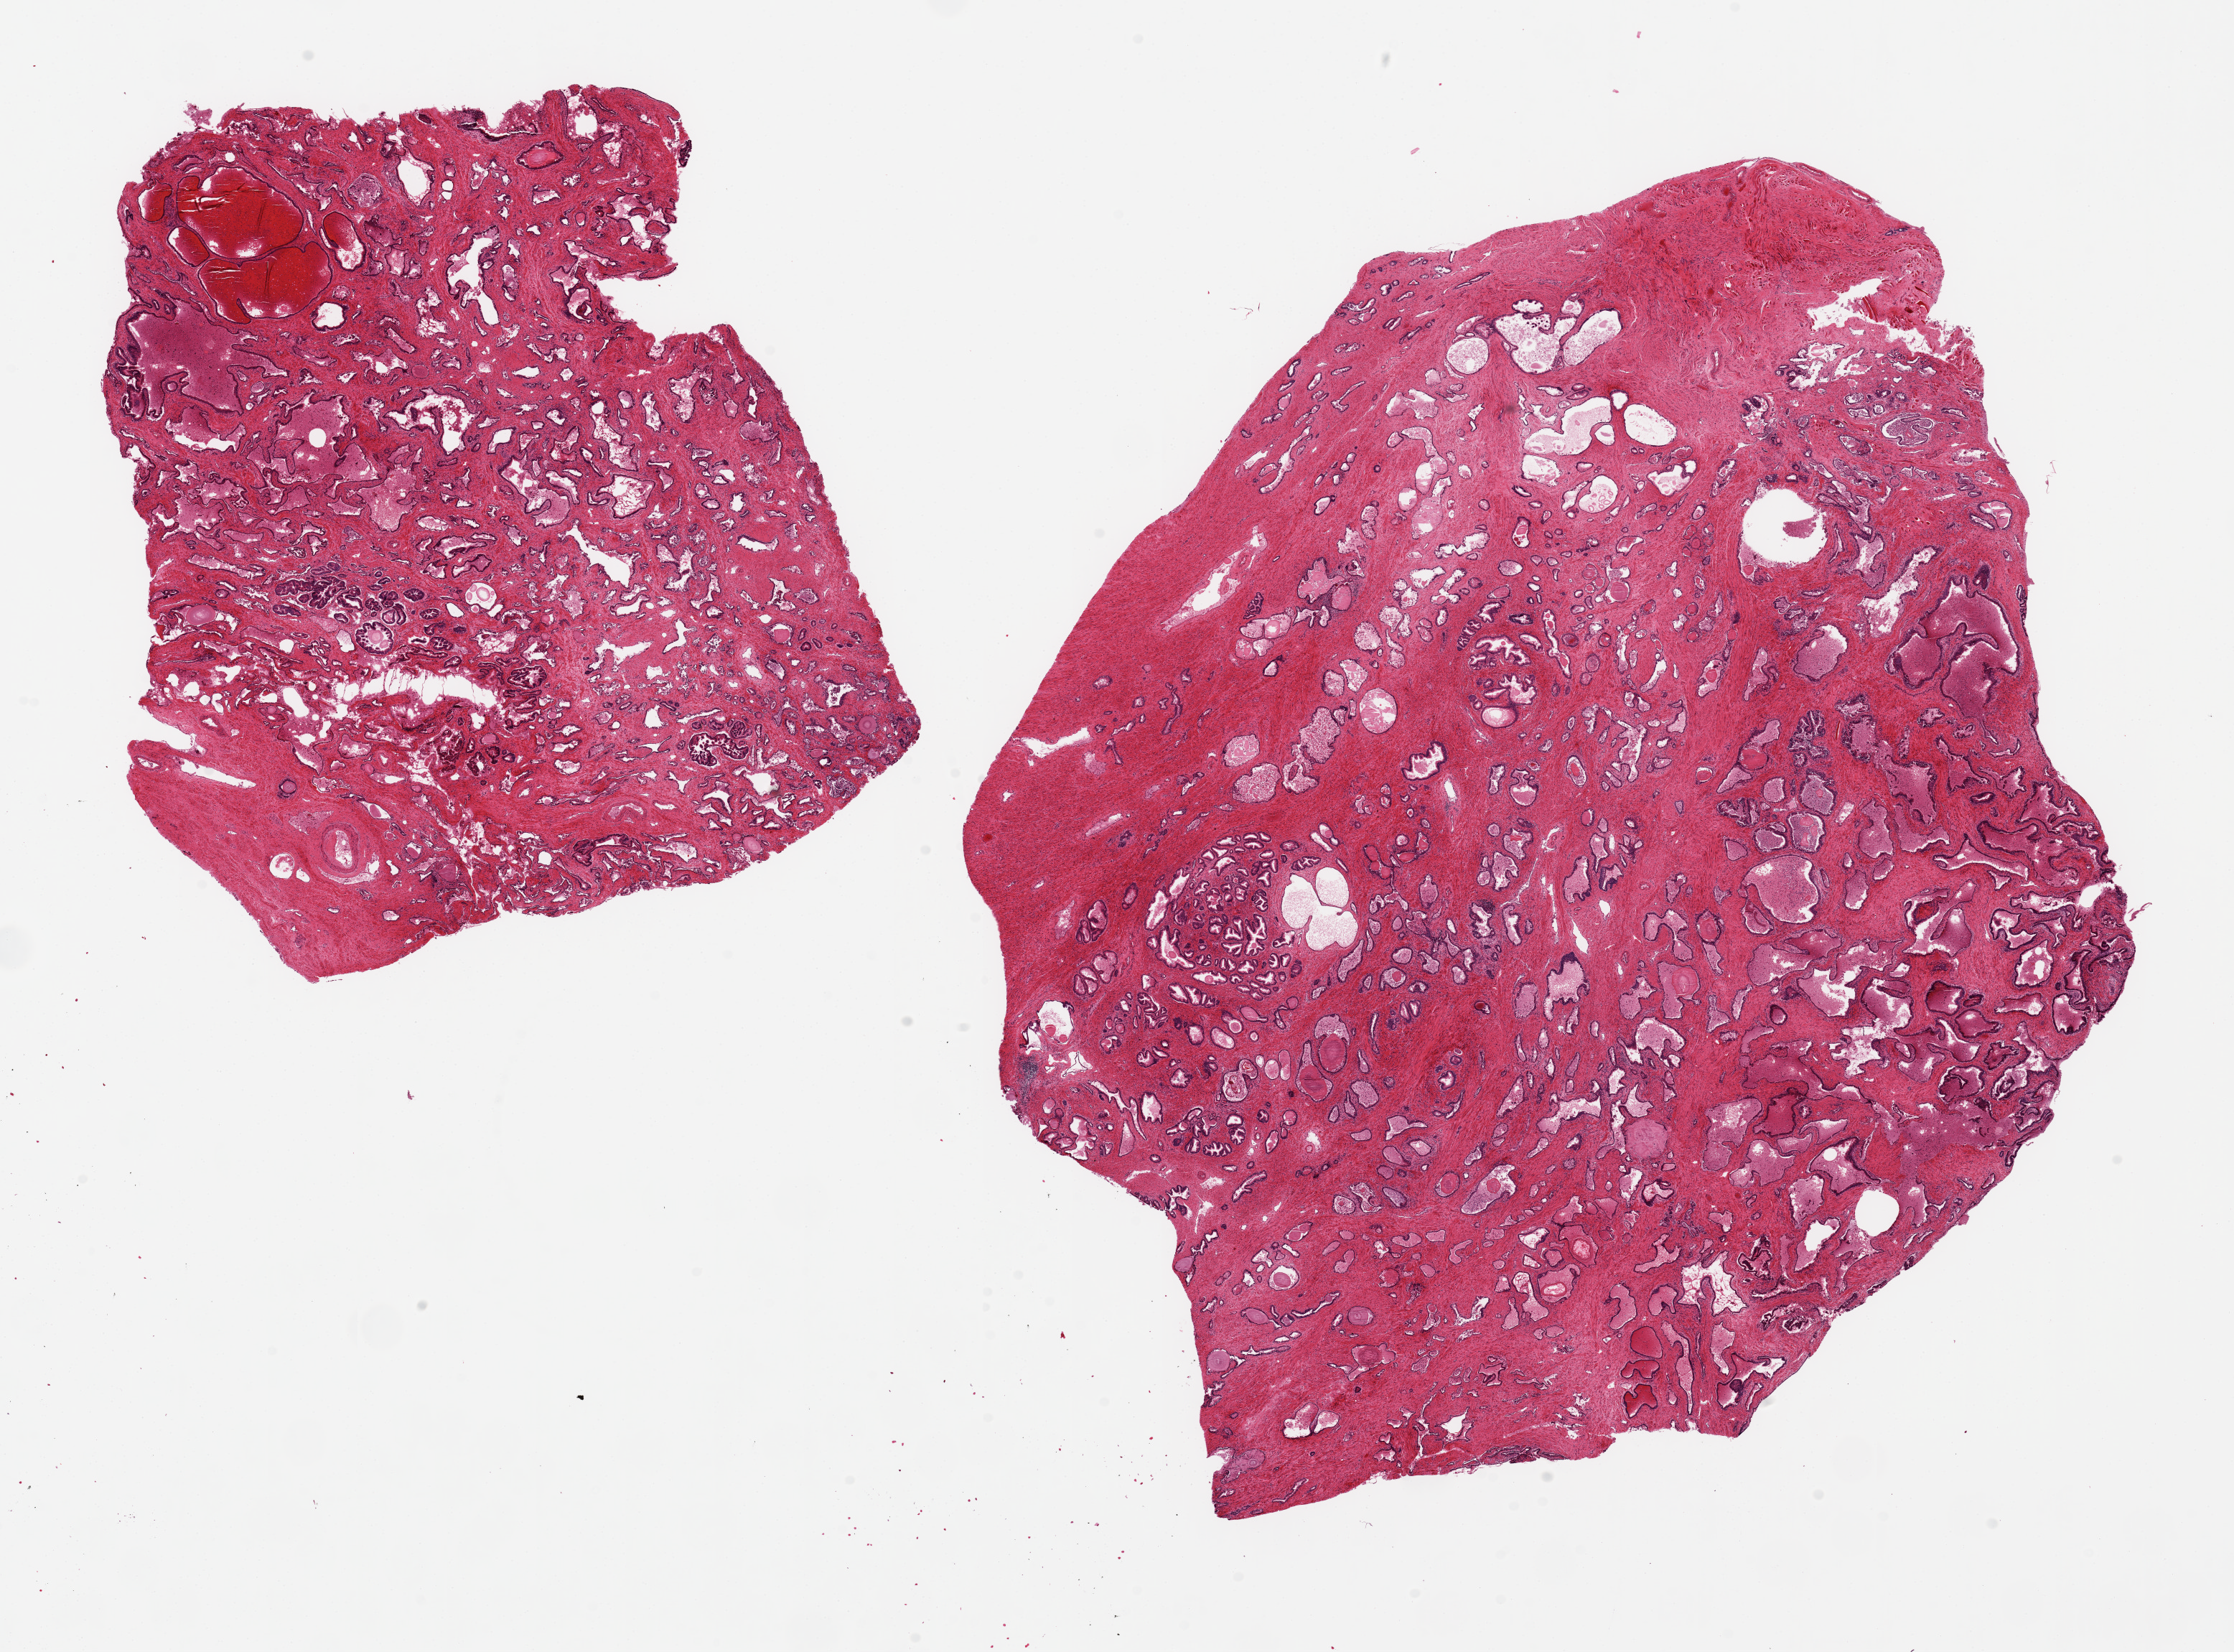
Digitized H&E-stained section, a low-resolution overview of the entire scanned area, about 24.6 x 18.2 mm (acquisition: 20x scan); PAXgene-fixed paraffin-embedded (PFPE) section; target tissue: prostate; donor tissue sample. Donor: male.
Review note (as recorded): 2 pieces ~10x8mm, glandular hyperplasia, focal PIN III, representative foc.